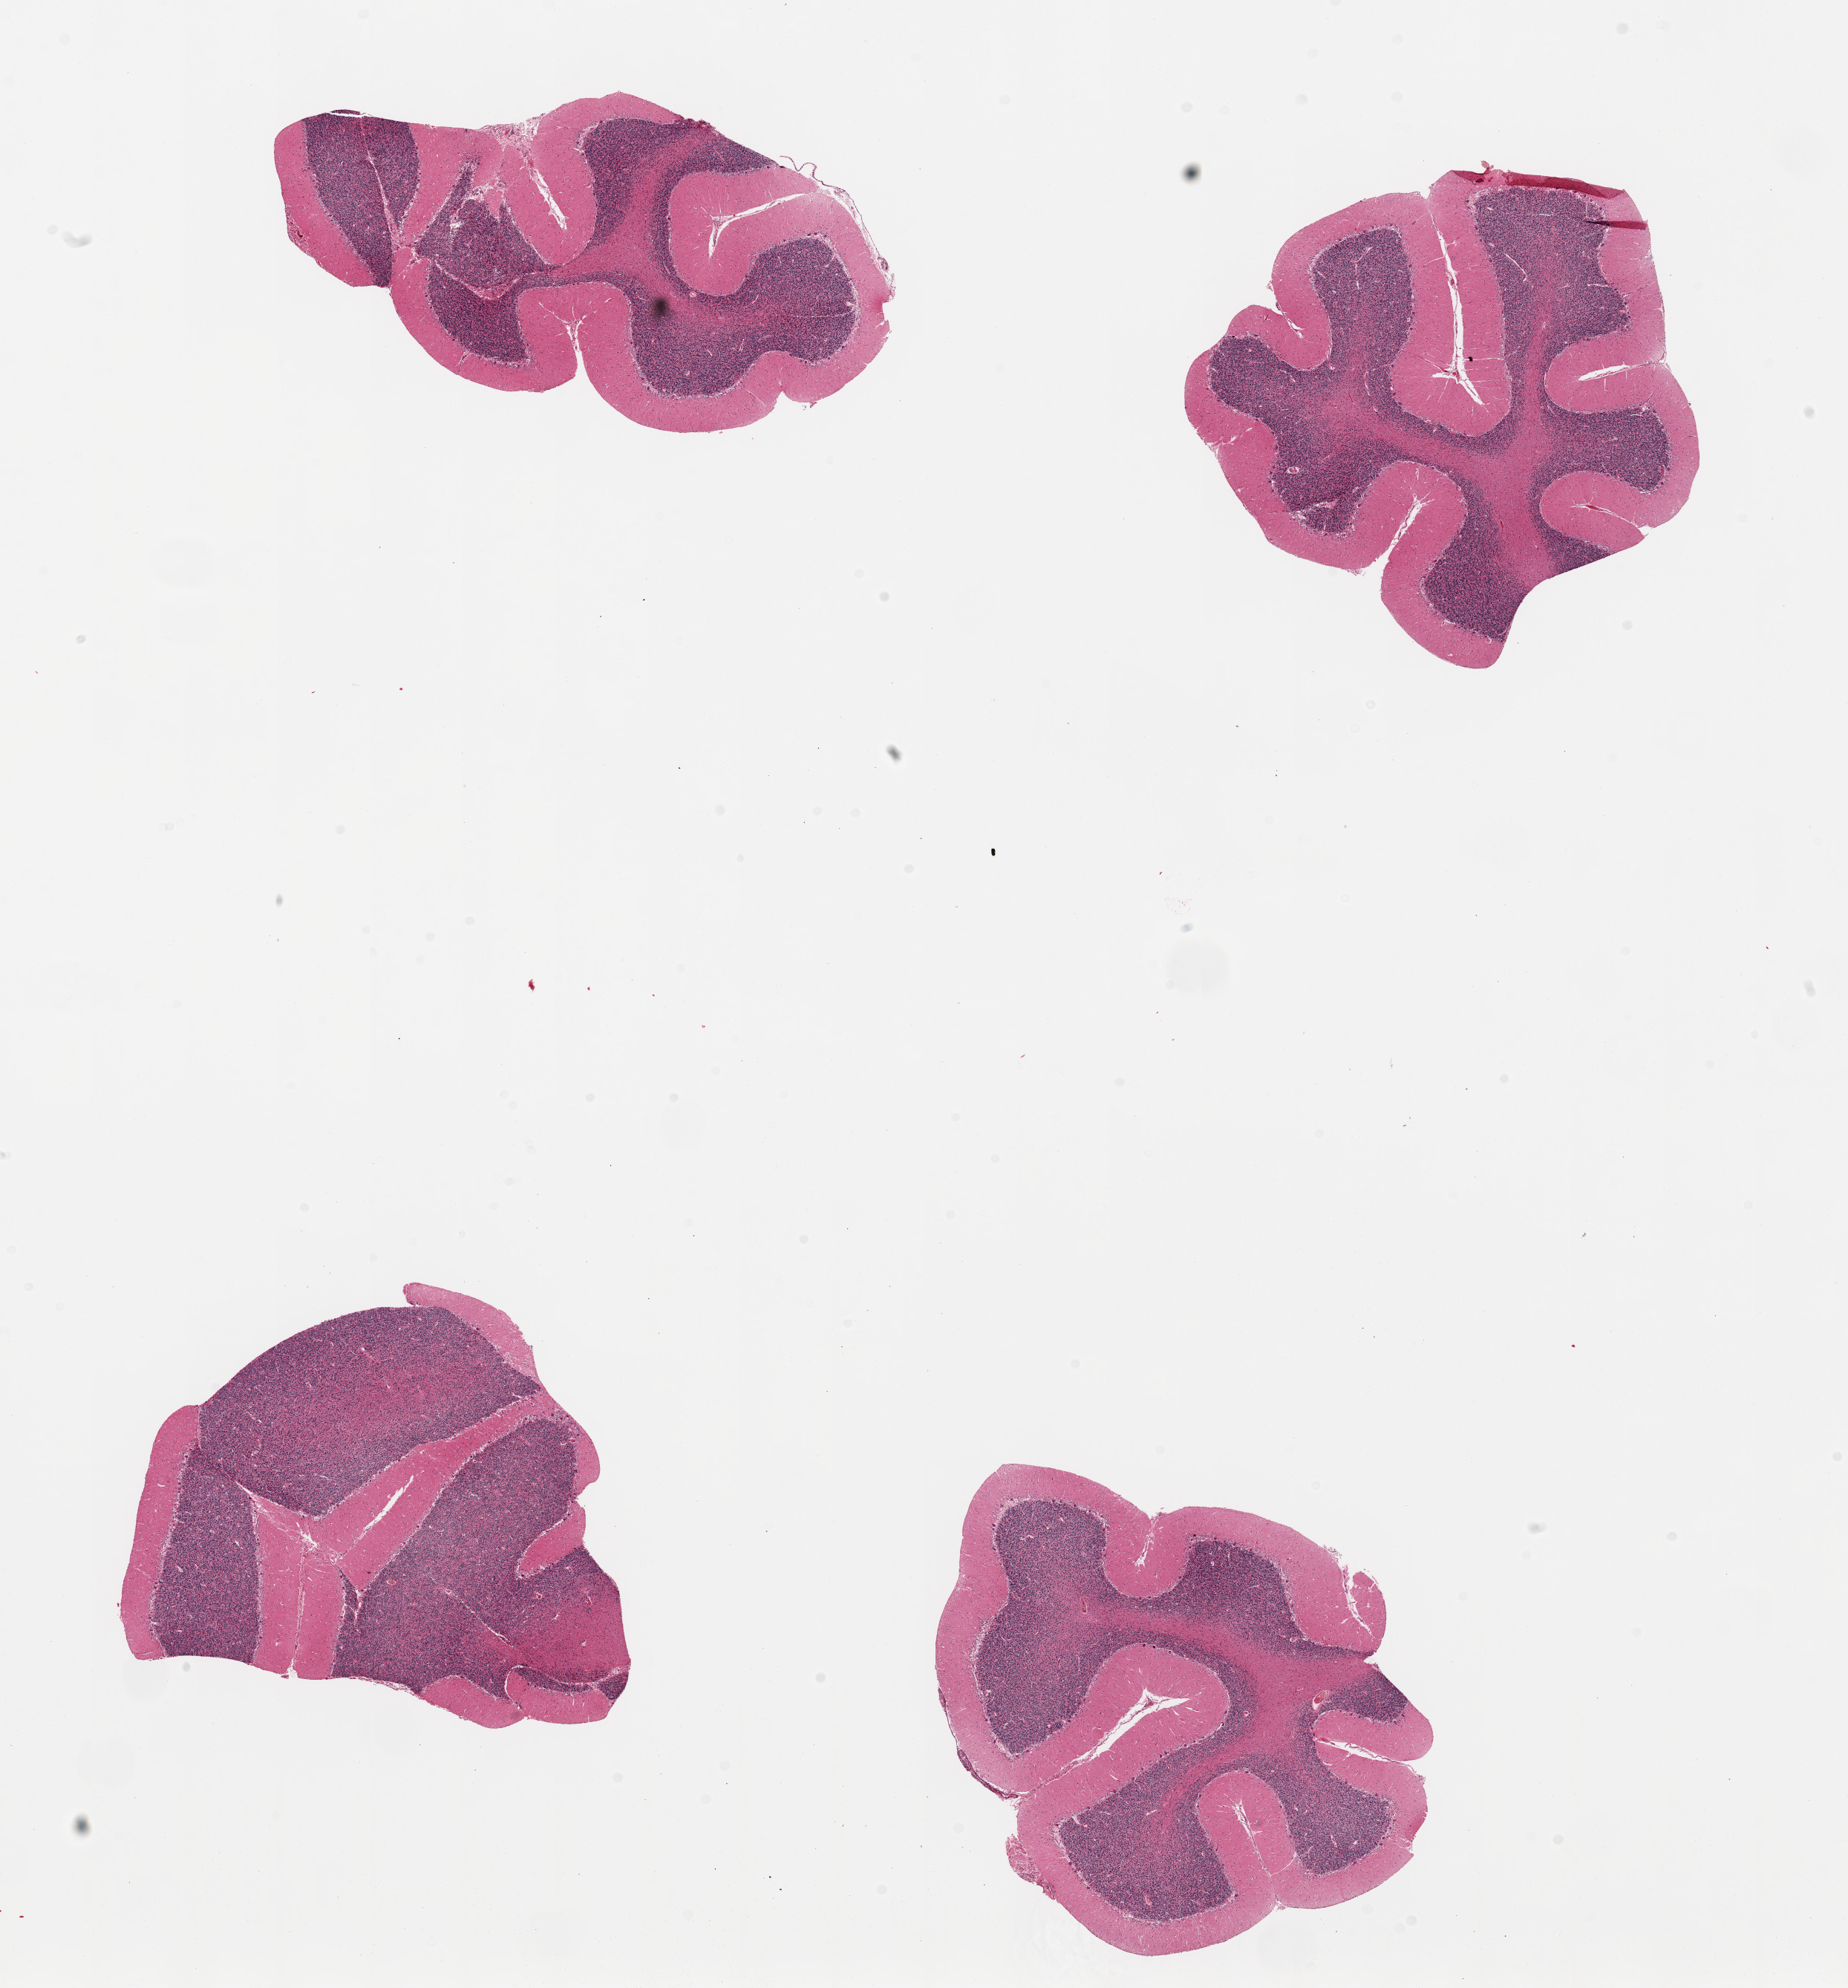
Digitized haematoxylin and eosin-stained section, brightfield, whole scanned area (about 19.7 x 21.2 mm) shown as a low-resolution overview, PAXgene-fixed, paraffin-embedded tissue, sampled site (target tissue): cerebellum, donor tissue sample. Female donor.
- reviewer comment on this tissue sample: 4 pieces